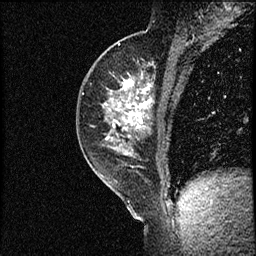
Breast MRI (dynamic contrast-enhanced), one sagittal slice; slice 33 of 56 in the series (ordered by position); dynamic contrast-enhanced study with each time point stored as its own series, time point 2 of 3 at this slice position (early post-contrast, ordered by acquisition time); 1.5 T; TE 4.2 ms, TR 17.3 ms; 2 mm slice thickness; 256 × 256 image matrix, field of view 200 × 200 mm. Female patient. Case-level facts recorded for this patient, not image findings: setting: breast cancer imaged before/during neoadjuvant chemotherapy; receptor status: HER2-positive.
Annotated regions visible in this slice (semi-automatic segmentation, software-assisted and operator-edited):
- analysis volume of interest (the breast-tissue region the enhancement analysis was run in; not a lesion): bounding box <76,50,156,155> (left, top, right, bottom; pixels)
- tumour enhancement mask (voxels above the 100 % enhancement threshold inside the analysis volume of interest): <113,78,152,130>